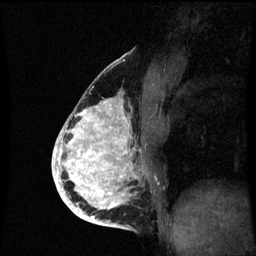
Breast MRI (dynamic contrast-enhanced), one sagittal slice. Position 34 of 60 along the scan axis. Dynamic contrast-enhanced series, image 2 of 3 at this slice position (ordered by acquisition). 1.5 T. TE 4.2 ms, TR 8.9 ms. 2 mm slice thickness. 256 × 256 image matrix, field of view 200 × 200 mm. Patient: female, 35 years. Case-level facts recorded for this patient, not image findings: setting: breast cancer imaged before/during neoadjuvant chemotherapy; receptor status: HR-positive, HER2-negative.
Structures marked on this image (semi-automatically segmented with operator editing):
- analysis volume of interest (the breast-tissue region the enhancement analysis was run in; not a lesion): bounding box (x1, y1, x2, y2) in pixels: (66, 94, 151, 215)
- tumour enhancement mask (voxels above the 70 % enhancement threshold inside the analysis volume of interest): (66, 98, 130, 215)